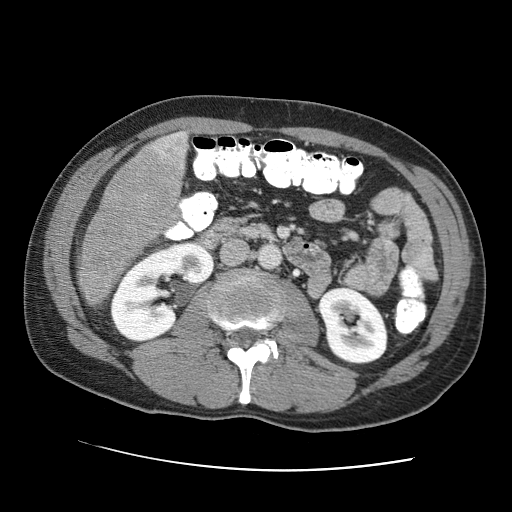
Contrast-enhanced abdominal CT (liver protocol), one axial slice. Slice 19 of 95 in the series (ordered by position). Reconstruction kernel STANDARD. One of 2 acquisitions stored at this slice position. Soft-tissue window (W 400 / L 40 HU). 2.5 mm slice thickness. 512 × 512 image matrix, field of view 360 × 360 mm. From the clinical record (not read from this slice): diagnosis: hepatocellular carcinoma (patient treated with transarterial chemoembolisation; whether this scan precedes or follows treatment is not stated here); TNM stage (as recorded): Stage-IVA; Child-Pugh class: A; tumour nodularity: multinodular.
Outlined on this slice (semi-automatically segmented with operator editing):
- liver parenchyma outside the tumour (the mass and vessels are separate outlines, so this box may not span the whole liver): box from (x=76, y=130) to (x=188, y=286) px
- mass: (x=76, y=133)–(x=184, y=308)
- liver vessels: (x=183, y=133)–(x=186, y=136)